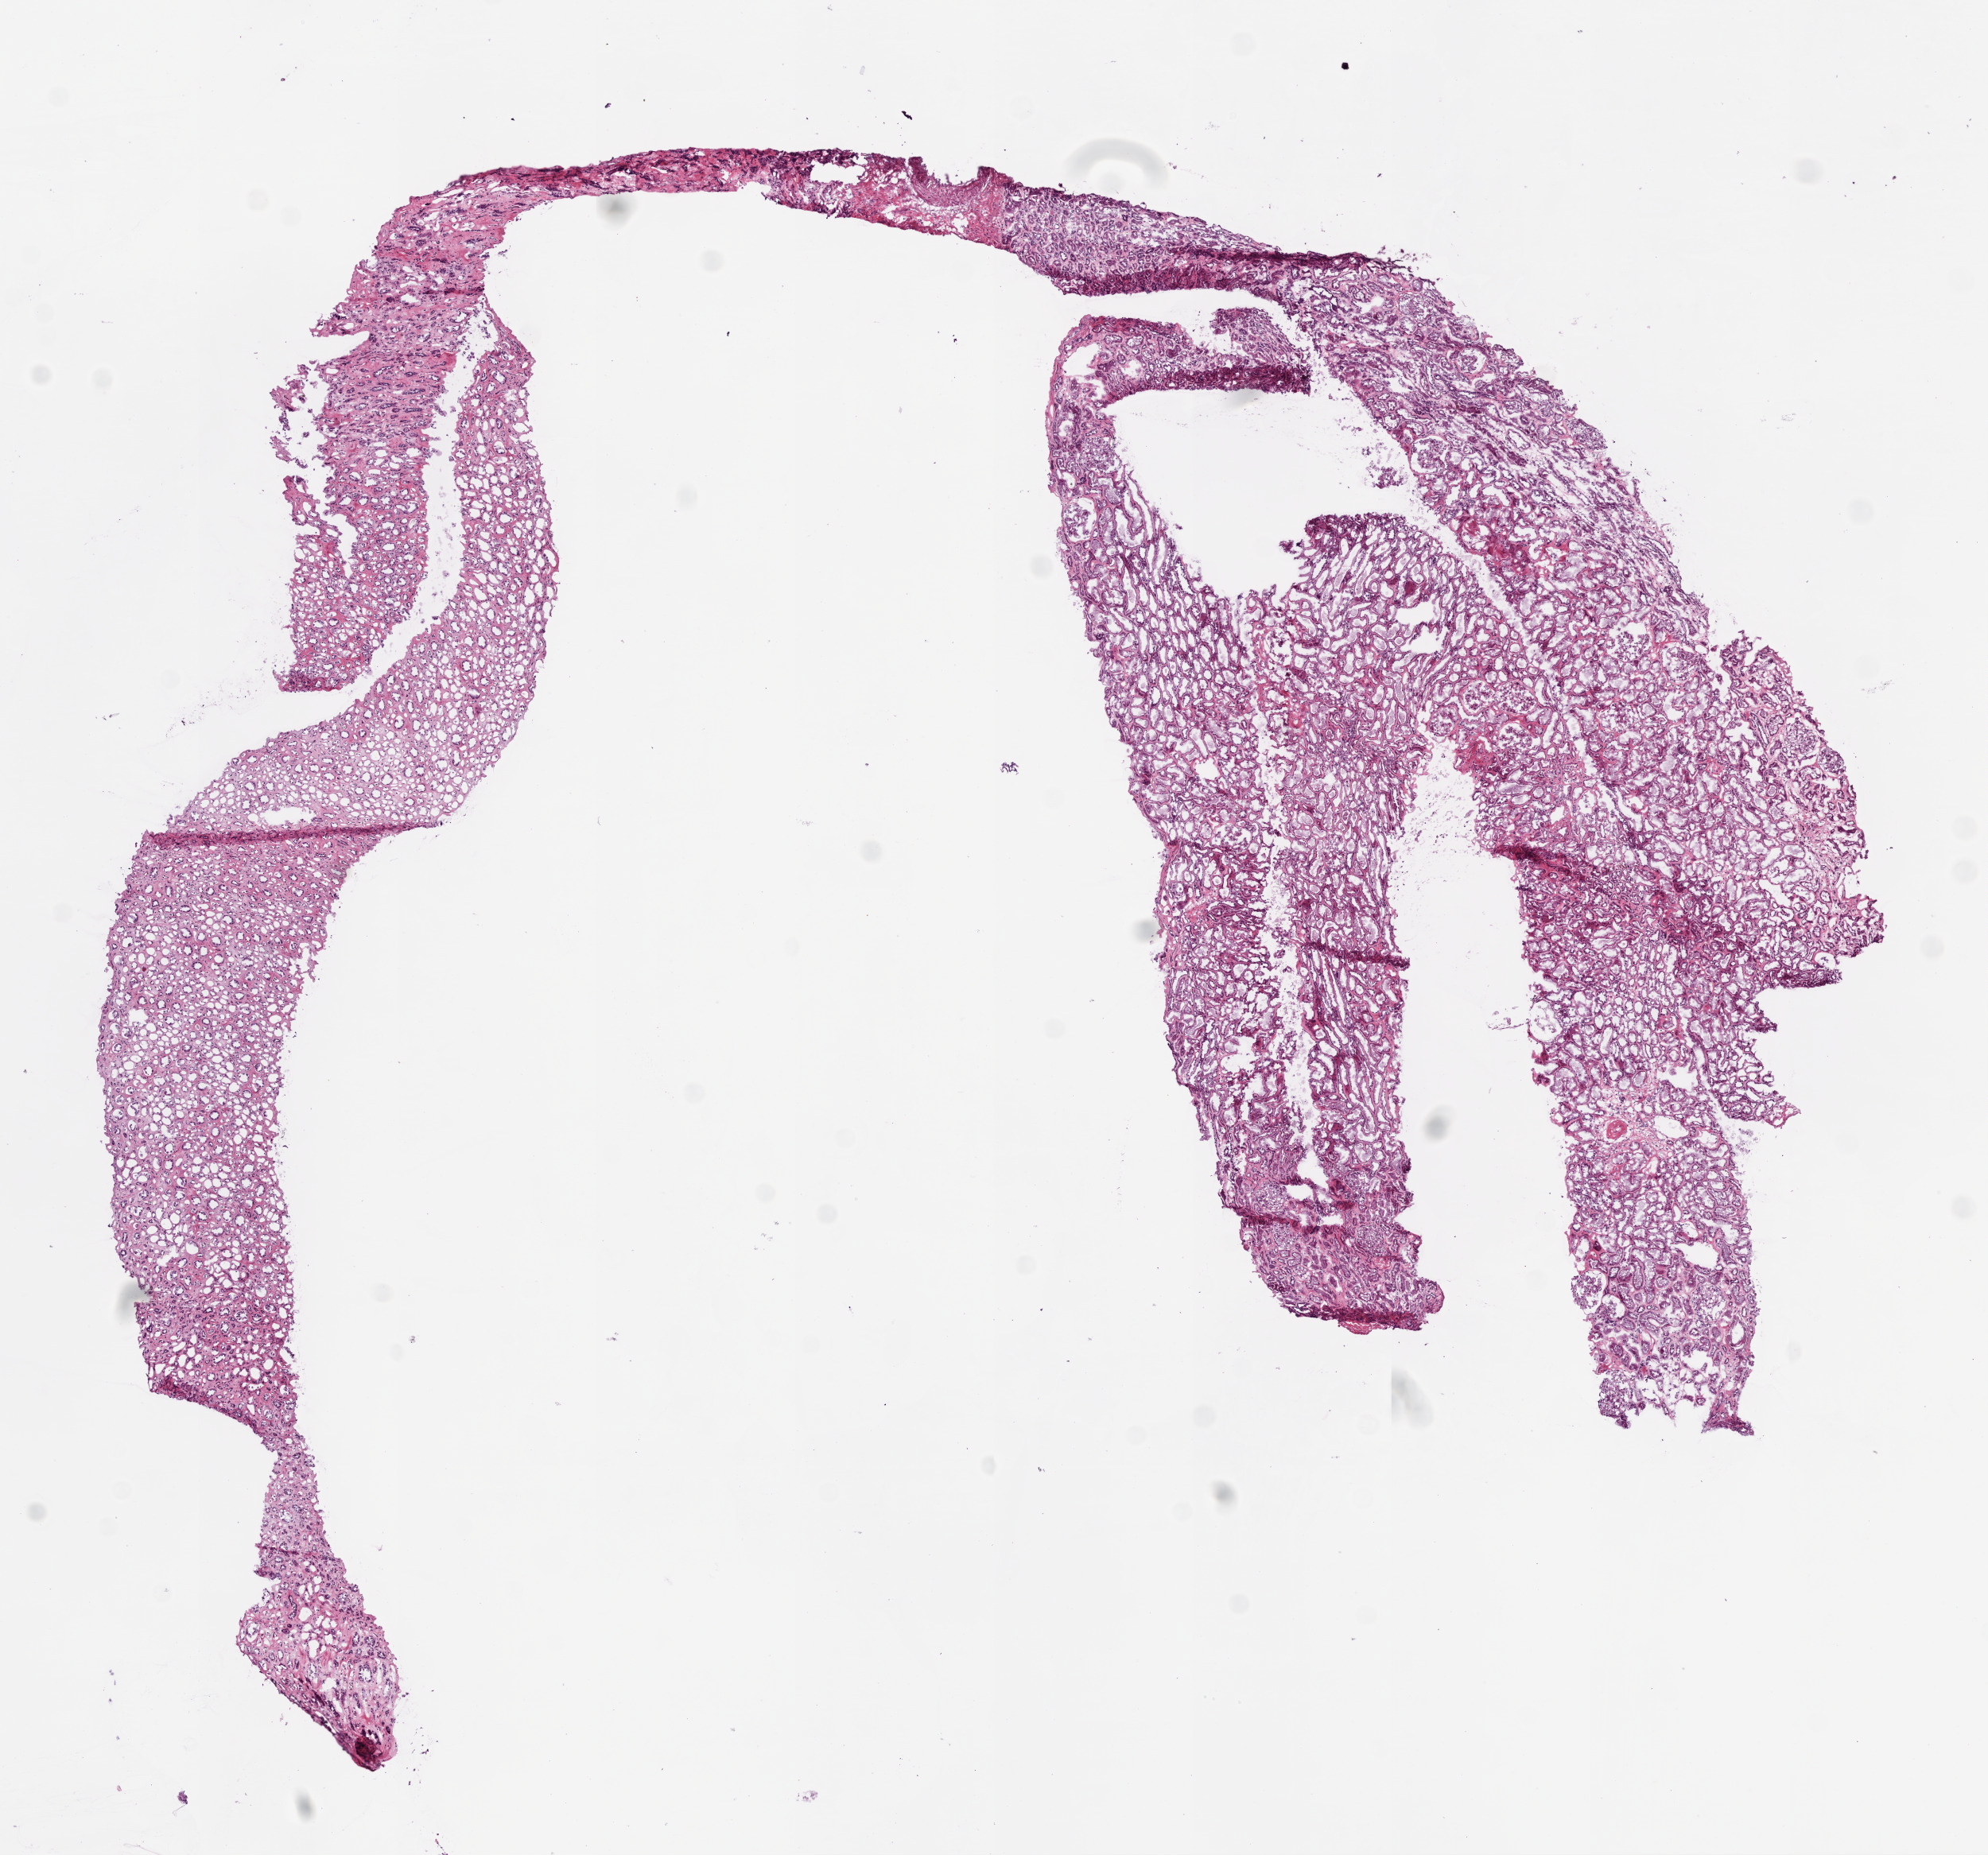
Hematoxylin and eosin (H&E) stained whole-slide image — a low-resolution overview of the entire scanned area, about 10.0 x 9.4 mm (acquisition: 20x scan), frozen section from the bottom of the tissue portion, sample: solid tissue normal (non-tumour tissue), kidney. Female, age 73 years at initial diagnosis.
* this section: solid tissue normal (non-tumour) sample from the same patient
* patient diagnosis: Clear cell adenocarcinoma, NOS